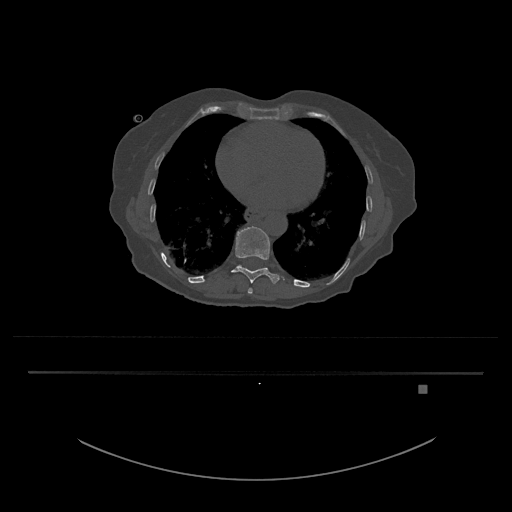
CT including the spine, one axial slice. Reconstruction kernel Br40s/3. Bone window (W 1800 / L 400 HU). 0.5 mm slice thickness. 512 × 512 image matrix, field of view 500 × 500 mm. Female patient, age 57 years. Case-level facts recorded for this patient, not image findings: primary cancer: cervical.
Annotated regions visible in this slice (semi-automatically segmented with operator editing):
- T10 vertebra: box from (x=231, y=226) to (x=283, y=284) px
- T9 vertebra: (x=247, y=288)–(x=253, y=294)